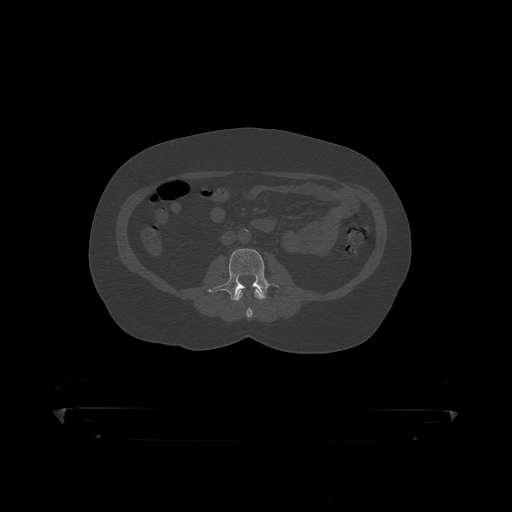
CT including the spine, one axial slice. Slice 96 of 390 in the series (ordered by position). Reconstruction kernel STANDARD. Bone window (W 1800 / L 400 HU). 1.25 mm slice thickness. 512 × 512 image matrix, field of view 650 × 650 mm. Male patient, age 60 years. Case-level facts recorded for this patient, not image findings: primary cancer: prostate.
Outlined on this slice (semi-automatic segmentation, software-assisted and operator-edited):
- L2 vertebra: bounding box [x1, y1, x2, y2] px = [236, 289, 264, 319]
- L3 vertebra: [208, 249, 279, 302]